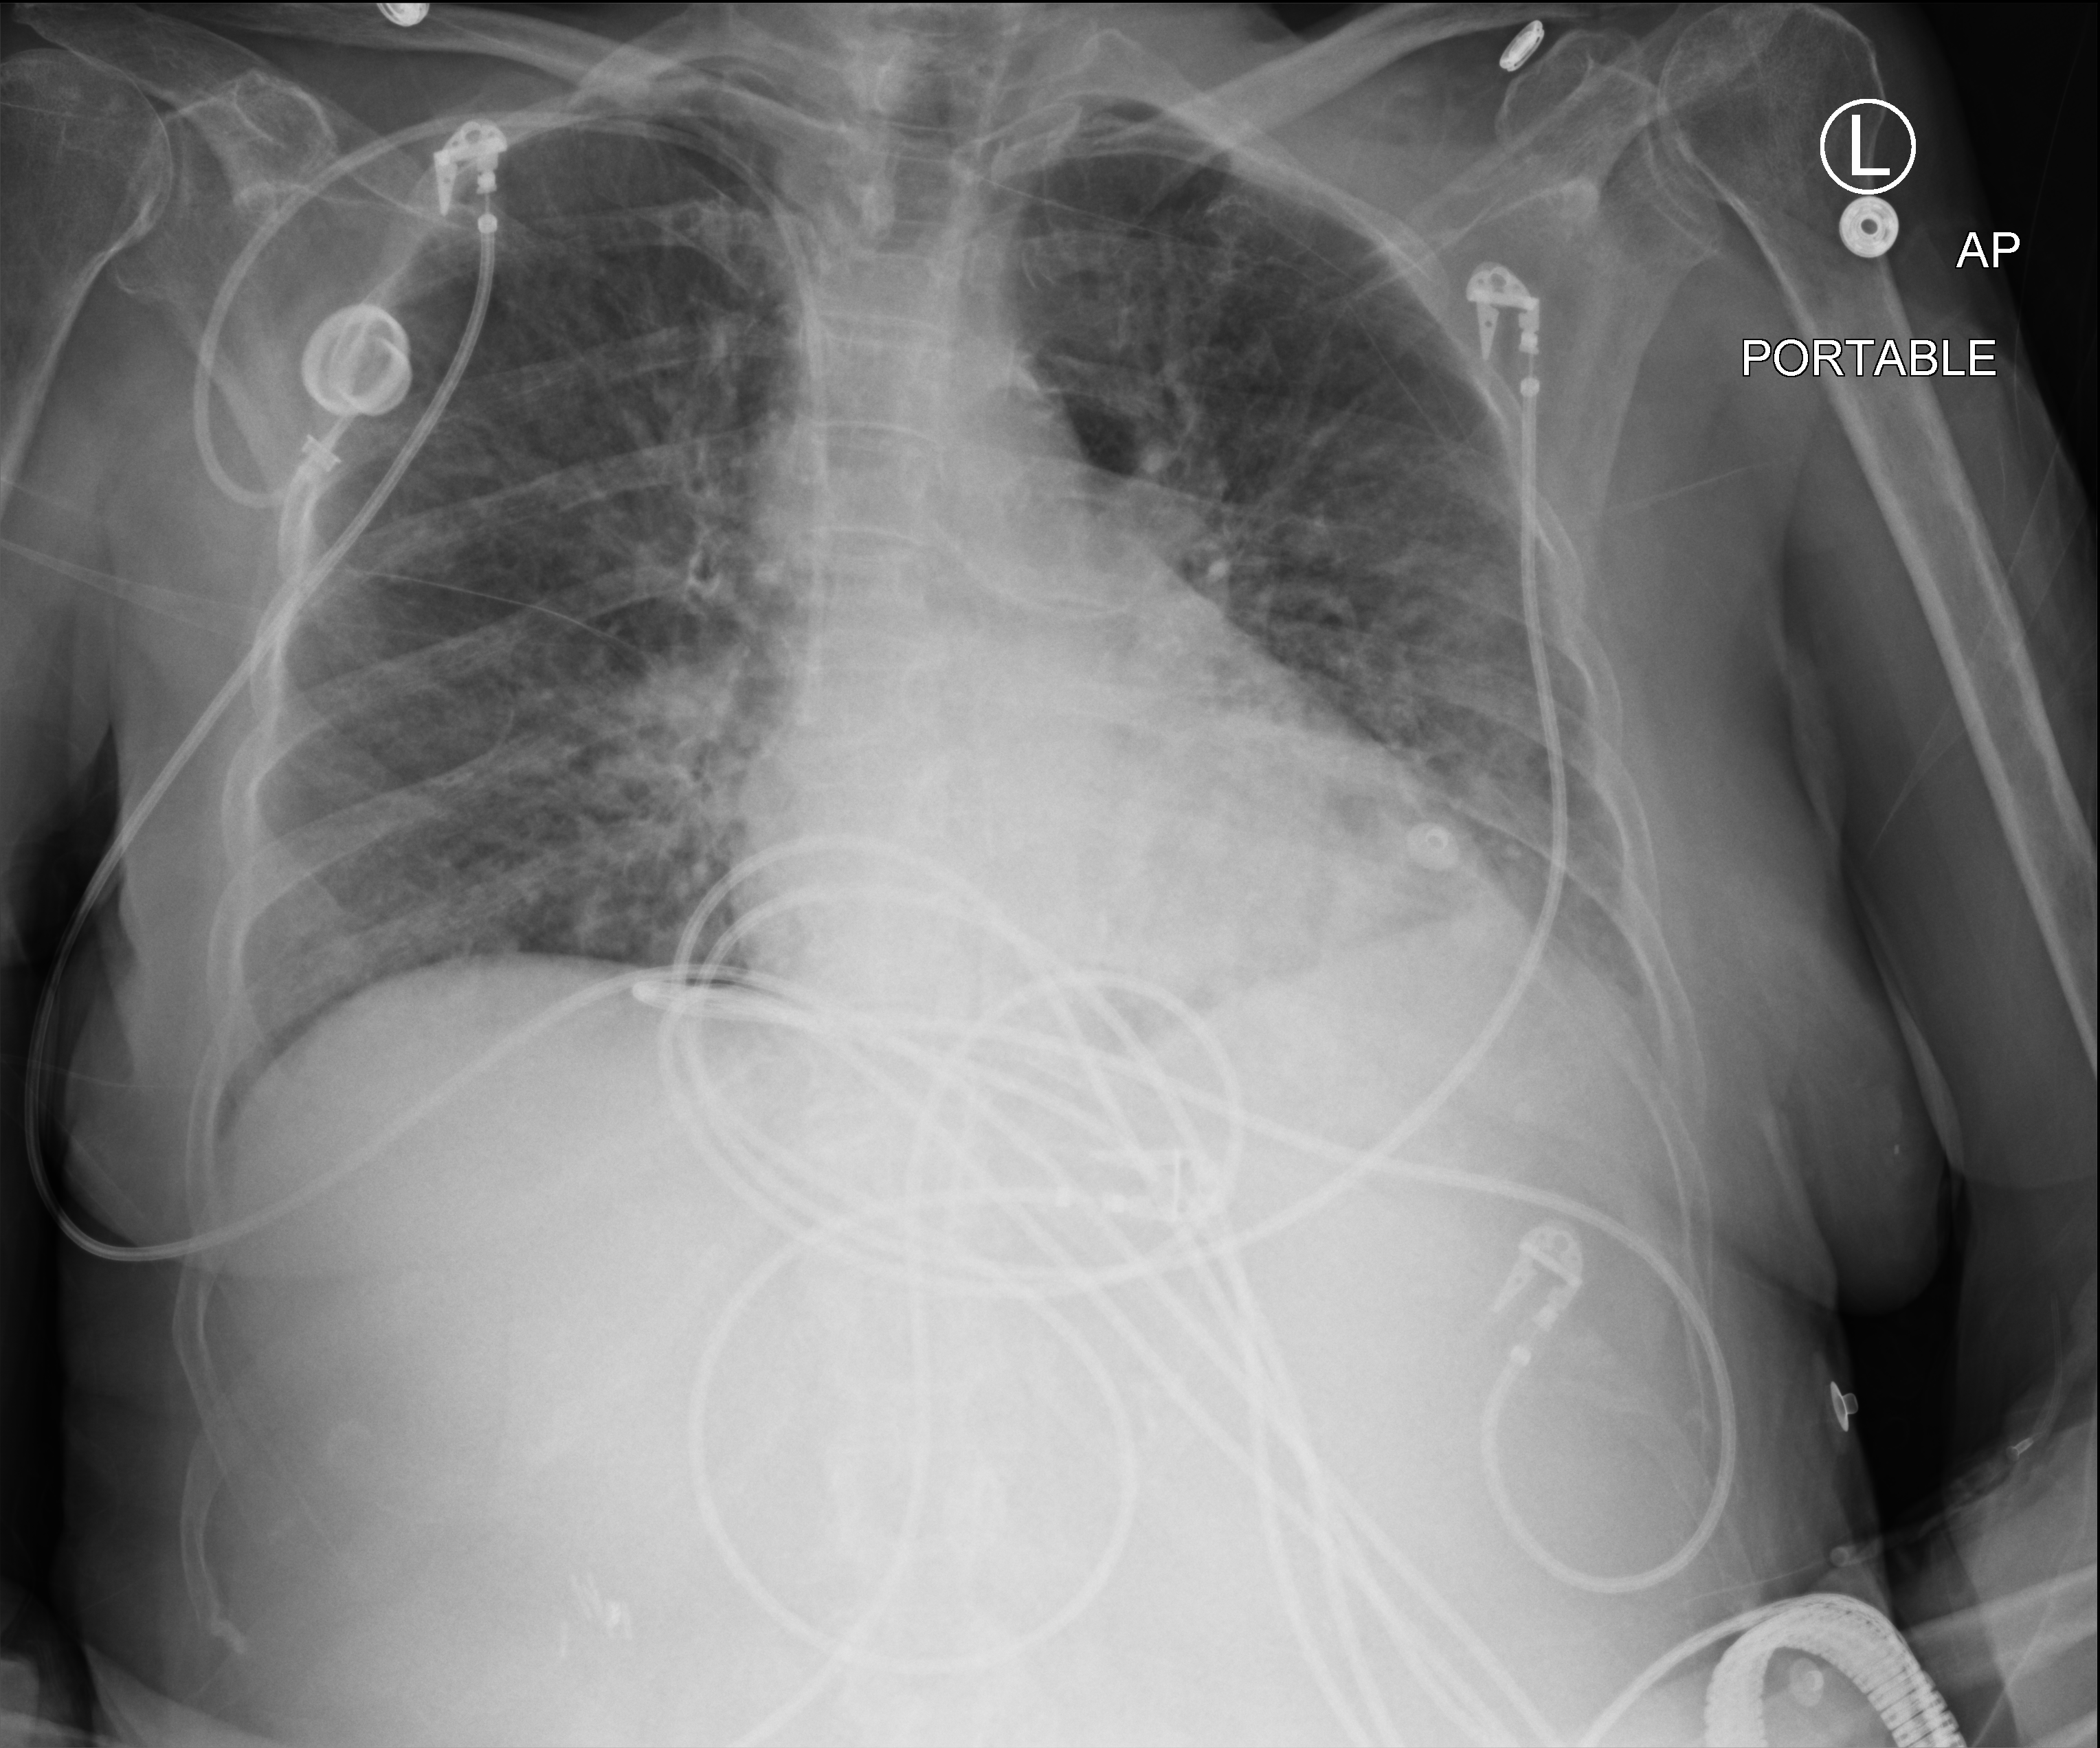
Bedside chest radiograph (computed radiography); anteroposterior (AP) projection. Female patient hospitalised with COVID-19, age 75–90 years.
Hospital-stay facts (about this admission, not read from this image; timing relative to this image not recorded): admitted to intensive care during this hospital stay: yes; length of hospital stay: 7 days; mechanically ventilated during this hospital stay: no.